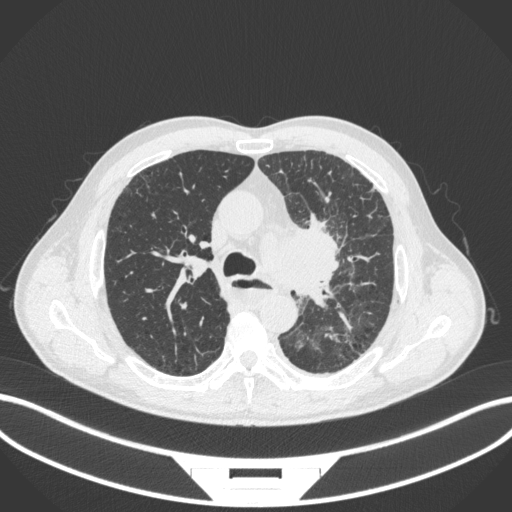
Chest CT, one axial slice; position 257 of 411 along the scan axis; reconstruction kernel B31f; lung window (W 1500 / L -600 HU); 1 mm slice thickness; 512 × 512 image matrix, field of view 400 × 400 mm. Patient: male, 57 years. From the clinical record (not read from this slice): clinical TNM (as recorded): T2a N1 M0.
Outlined on this slice (rectangle marked by the reading radiologist):
- lung tumour (recorded histology: squamous cell carcinoma): box from (x=258, y=221) to (x=346, y=300) px